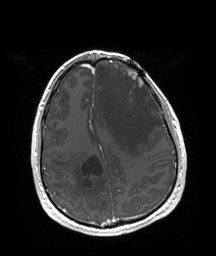
Brain MRI from a brain-tumour surgery series, one axial slice; slice 59 of 192 in the series (ordered by position); T1-weighted post-contrast; 216 × 256 image matrix, field of view 219 × 260 mm. From the clinical record (not read from this slice): tumour location: Left Frontal.
Annotated regions visible in this slice (manually delineated by an expert):
- tumour: bounding box (x1, y1, x2, y2) in pixels: (124, 67, 143, 87)